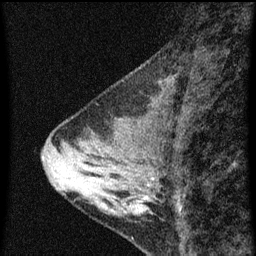
Breast MRI (dynamic contrast-enhanced), one sagittal slice. Slice 24 of 60 in the series (ordered by position). Dynamic contrast-enhanced series, image 2 of 3 at this slice position (ordered by acquisition). 1.5 T. TE 4.2 ms, TR 8 ms. 2 mm slice thickness. 256 × 256 image matrix, field of view 180 × 180 mm. Patient: female, 34 years.
Annotated regions visible in this slice (semi-automatically segmented with operator editing):
- analysis volume of interest (the breast-tissue region the enhancement analysis was run in; not a lesion): bounding box <70,138,161,223> (left, top, right, bottom; pixels)
- tumour enhancement mask (voxels above the 70 % enhancement threshold inside the analysis volume of interest): <146,196,149,199>